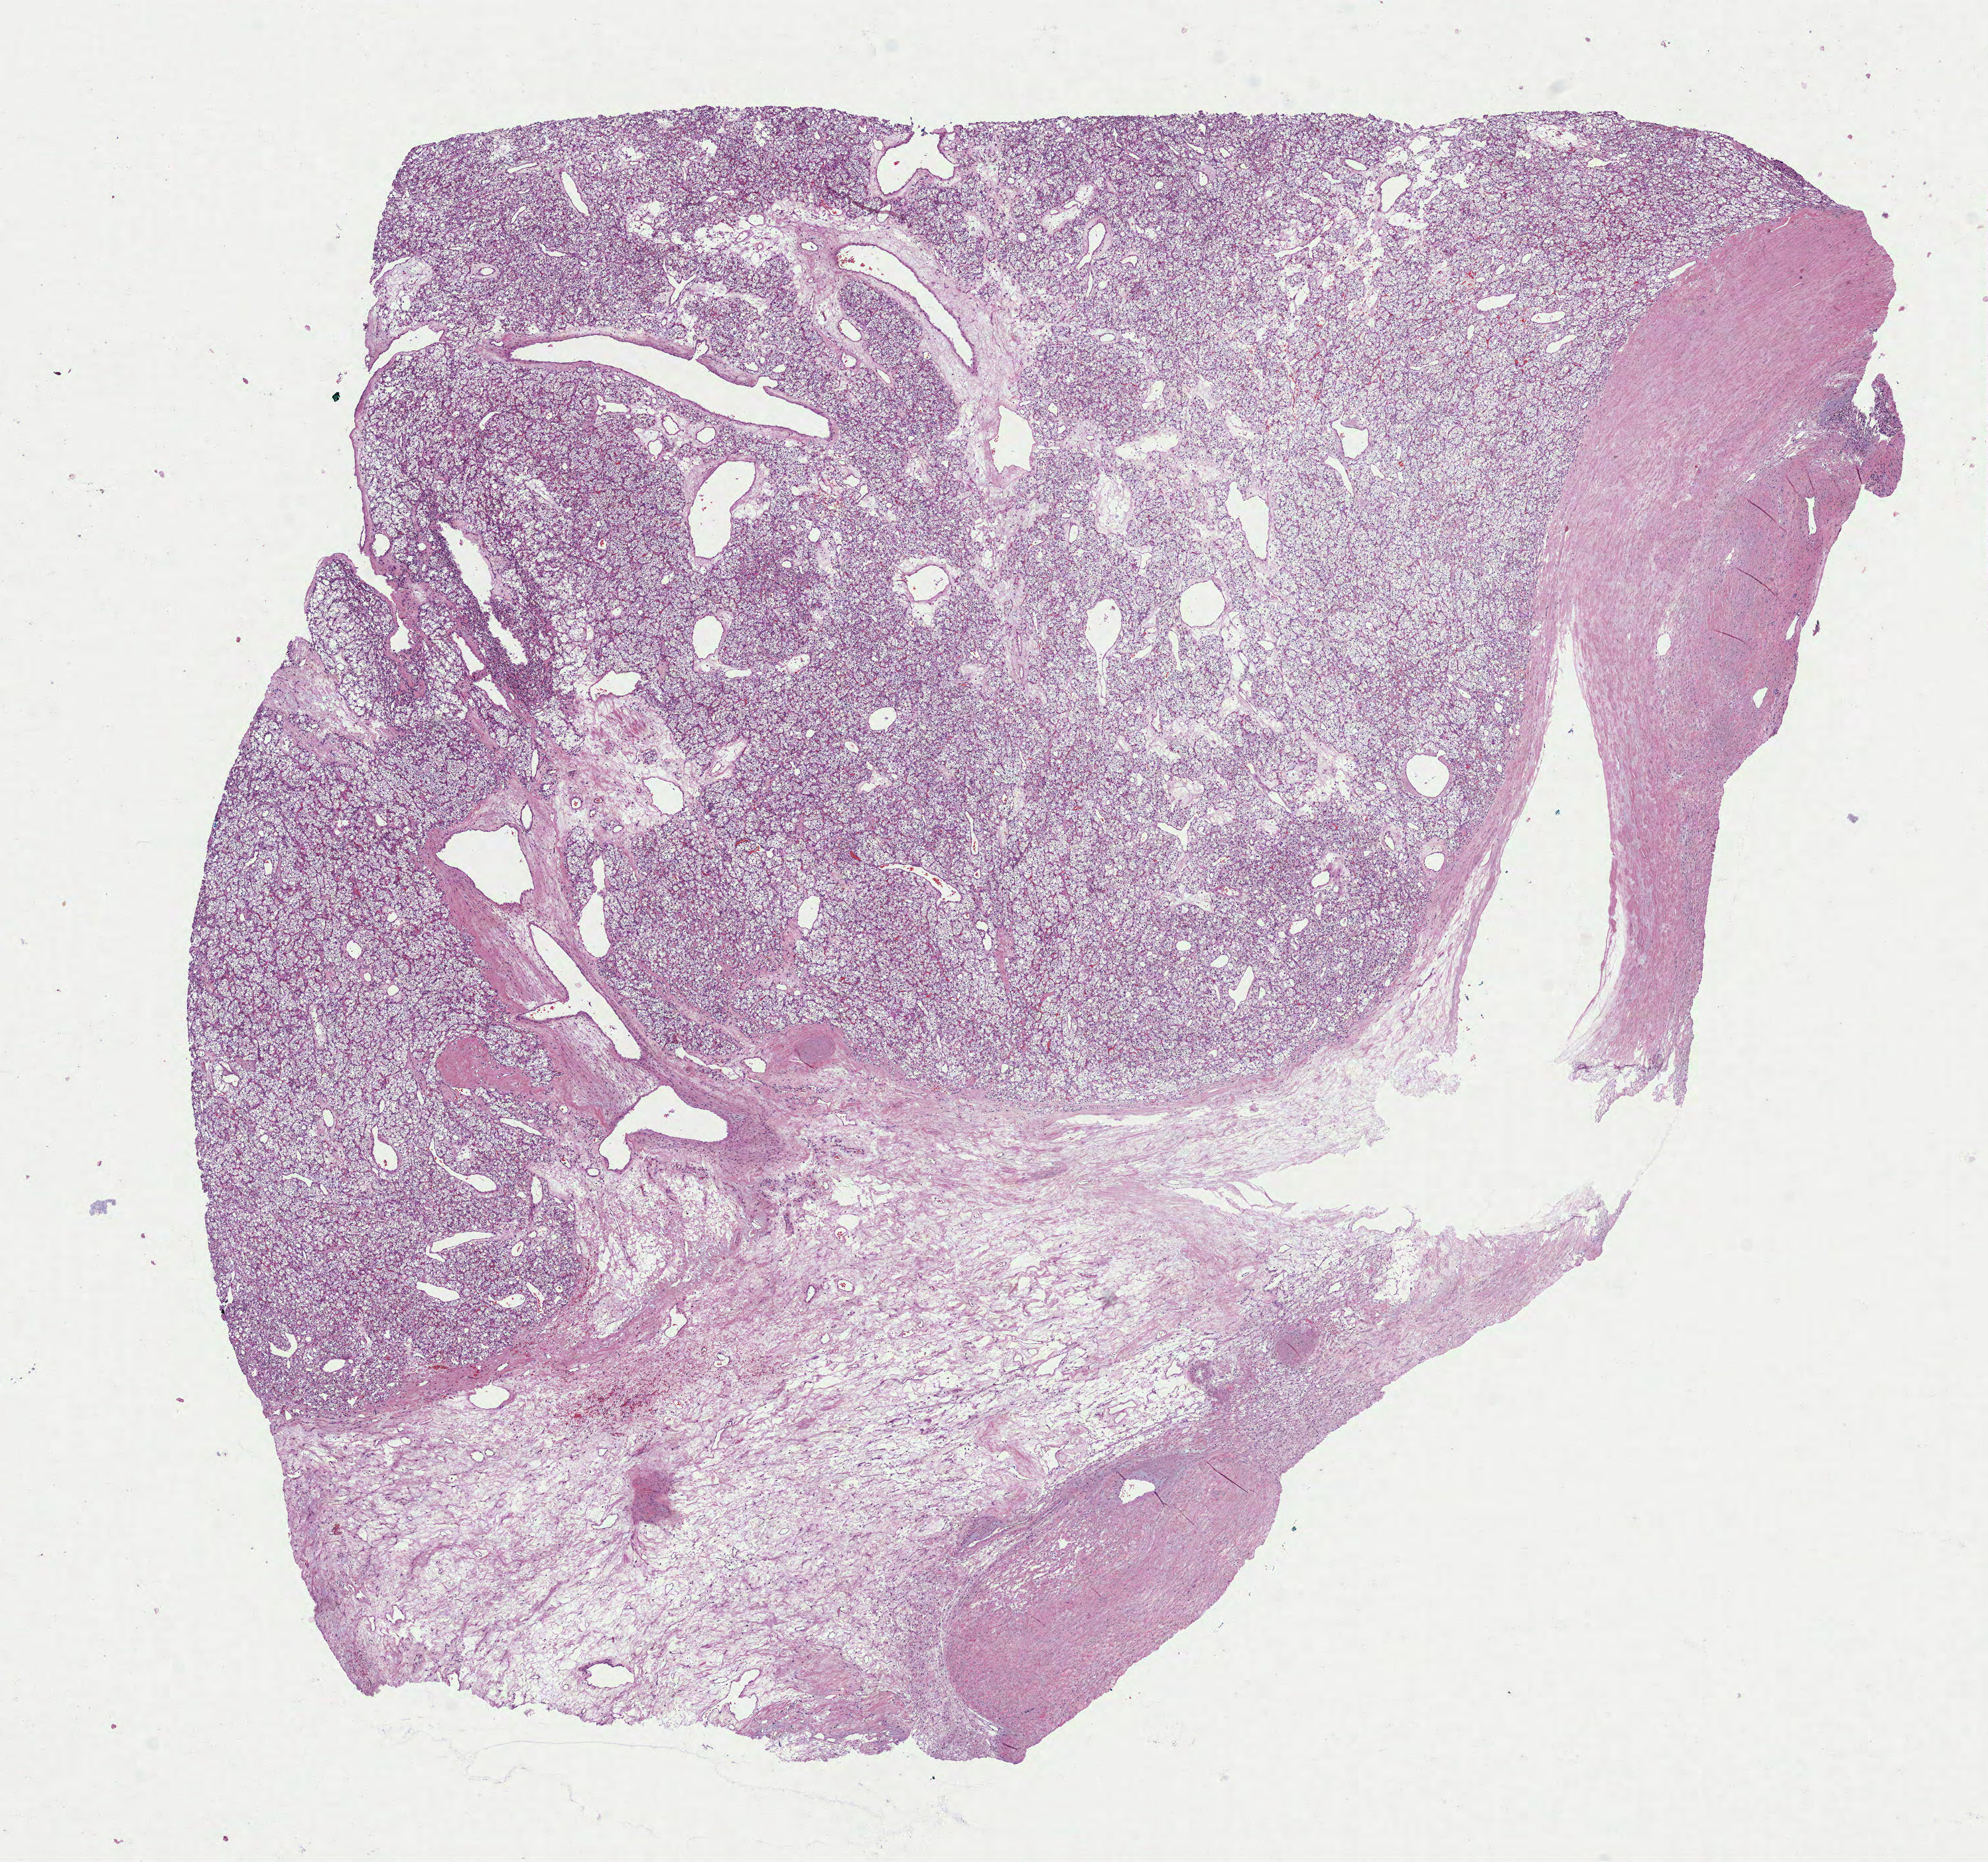
Digitized H&E-stained tissue section (whole slide) — a low-resolution overview of the entire scanned area, about 12.1 x 11.3 mm (acquisition: 40x scan). Formalin-fixed paraffin-embedded (FFPE) diagnostic section. Primary tumour sample from the kidney. Male patient; age at initial diagnosis 37 years. Histologic grade: G2 (moderately differentiated).
Diagnosis: Clear cell adenocarcinoma, NOS. AJCC pathologic stage: III (7th edition). TNM: T3a NX MX.